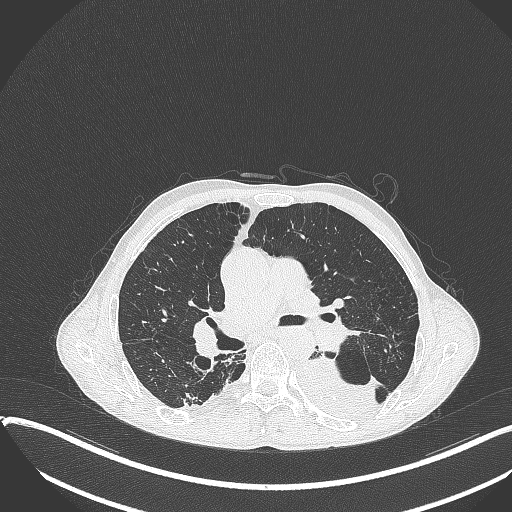
Chest CT, one axial slice; slice 226 of 401 in the series (ordered by position); reconstruction kernel B70f; lung window (W 1500 / L -600 HU); 1 mm slice thickness; 512 × 512 image matrix. Male patient, age 57 years. From the clinical record (not read from this slice): clinical TNM (as recorded): T4 N0 M0.
Annotated regions visible in this slice (rectangle marked by the reading radiologist):
- lung tumour (recorded histology: squamous cell carcinoma): box from (x=292, y=352) to (x=389, y=421) px